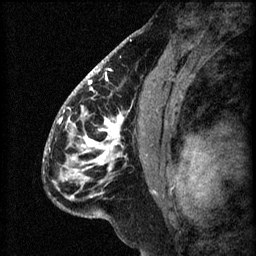
Breast MRI (dynamic contrast-enhanced), one sagittal slice; position 36 of 60 along the scan axis; 3 images stored at this slice position (order not interpretable as contrast timing); 1.5 T; TE 4.2 ms, TR 8.2 ms; 2.2 mm slice thickness; 256 × 256 image matrix, field of view 180 × 180 mm. Female patient, age 41 years.
Structures marked on this image (semi-automatically segmented with operator editing):
- analysis volume of interest (the breast-tissue region the enhancement analysis was run in; not a lesion): bounding box <56,104,157,207> (left, top, right, bottom; pixels)
- tumour enhancement mask (voxels above the 70 % enhancement threshold inside the analysis volume of interest): <61,106,124,199>